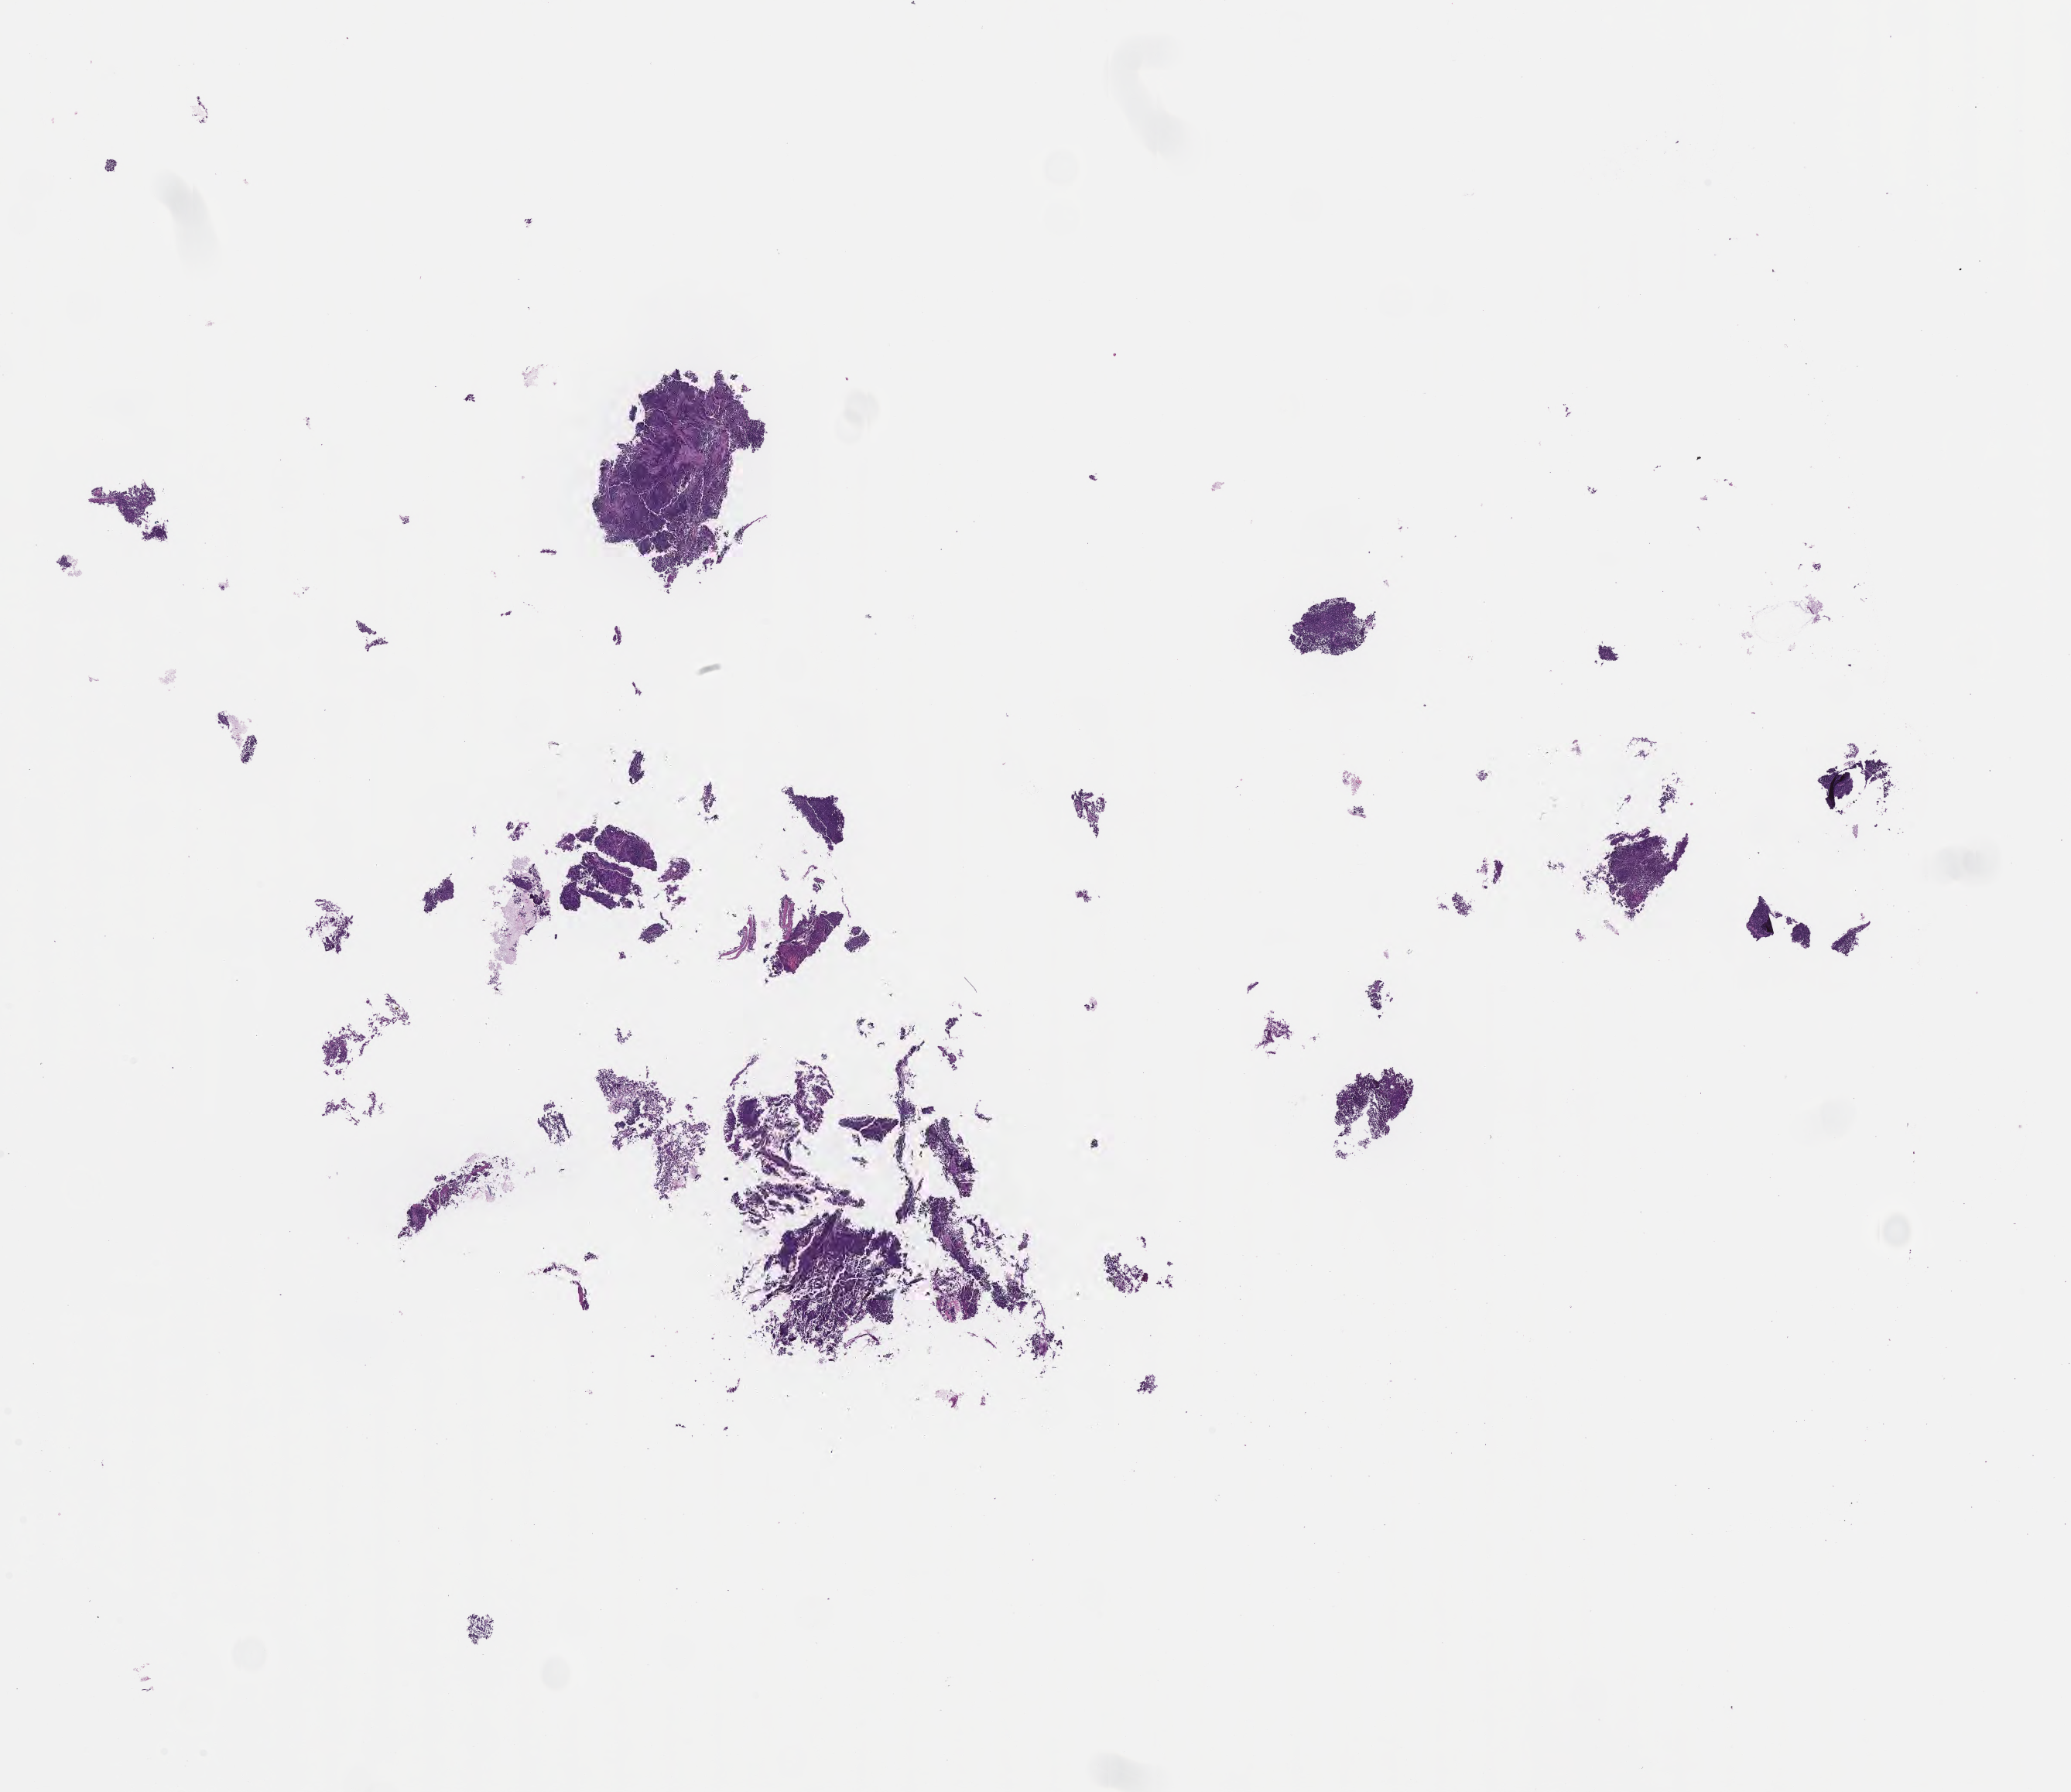
Haematoxylin and eosin whole-slide image of tumor tissue from the cerebellum, whole scanned area (about 21.6 x 18.7 mm) shown as a low-resolution overview. FFPE section. Male patient, age 687 days (about 1.9 years).
• diagnosis (ICD-O-3 morphology term): Medulloblastoma, NOS